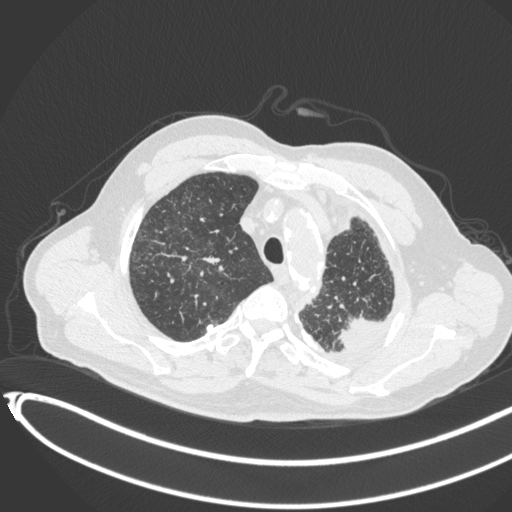
Chest CT, one axial slice; slice 348 of 451 in the series (ordered by position); reconstruction kernel B31f; lung window (W 1500 / L -600 HU); 1 mm slice thickness; 512 × 512 image matrix, field of view 400 × 400 mm. Male patient, age 78 years. From the clinical record (not read from this slice): clinical TNM (as recorded): T1c N0 M1.
Outlined on this slice (rectangle marked by the reading radiologist):
- lung tumour (recorded histology: adenocarcinoma): bounding box (x1, y1, x2, y2) in pixels: (333, 305, 387, 354)